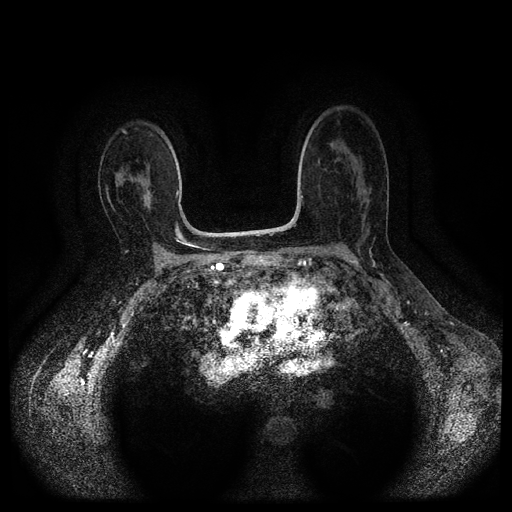
Breast MRI (dynamic contrast-enhanced, multi-phase), one axial slice. Slice 58 of 112 in the series (ordered by position). Dynamic contrast-enhanced series, time point 2 of 5 at this slice position (early post-contrast). 1.5 T. TE 2.6 ms, TR 5.4 ms. 2 mm slice thickness. 512 × 512 image matrix, field of view 340 × 340 mm. Female patient, age 53 years.
Structures marked on this image (semi-automatic segmentation, software-assisted and operator-edited):
- breast lesion (labelled 'tumour' in the annotation; benign lesions carry a separate 'benign' label): bounding box <134,178,151,212> (left, top, right, bottom; pixels)